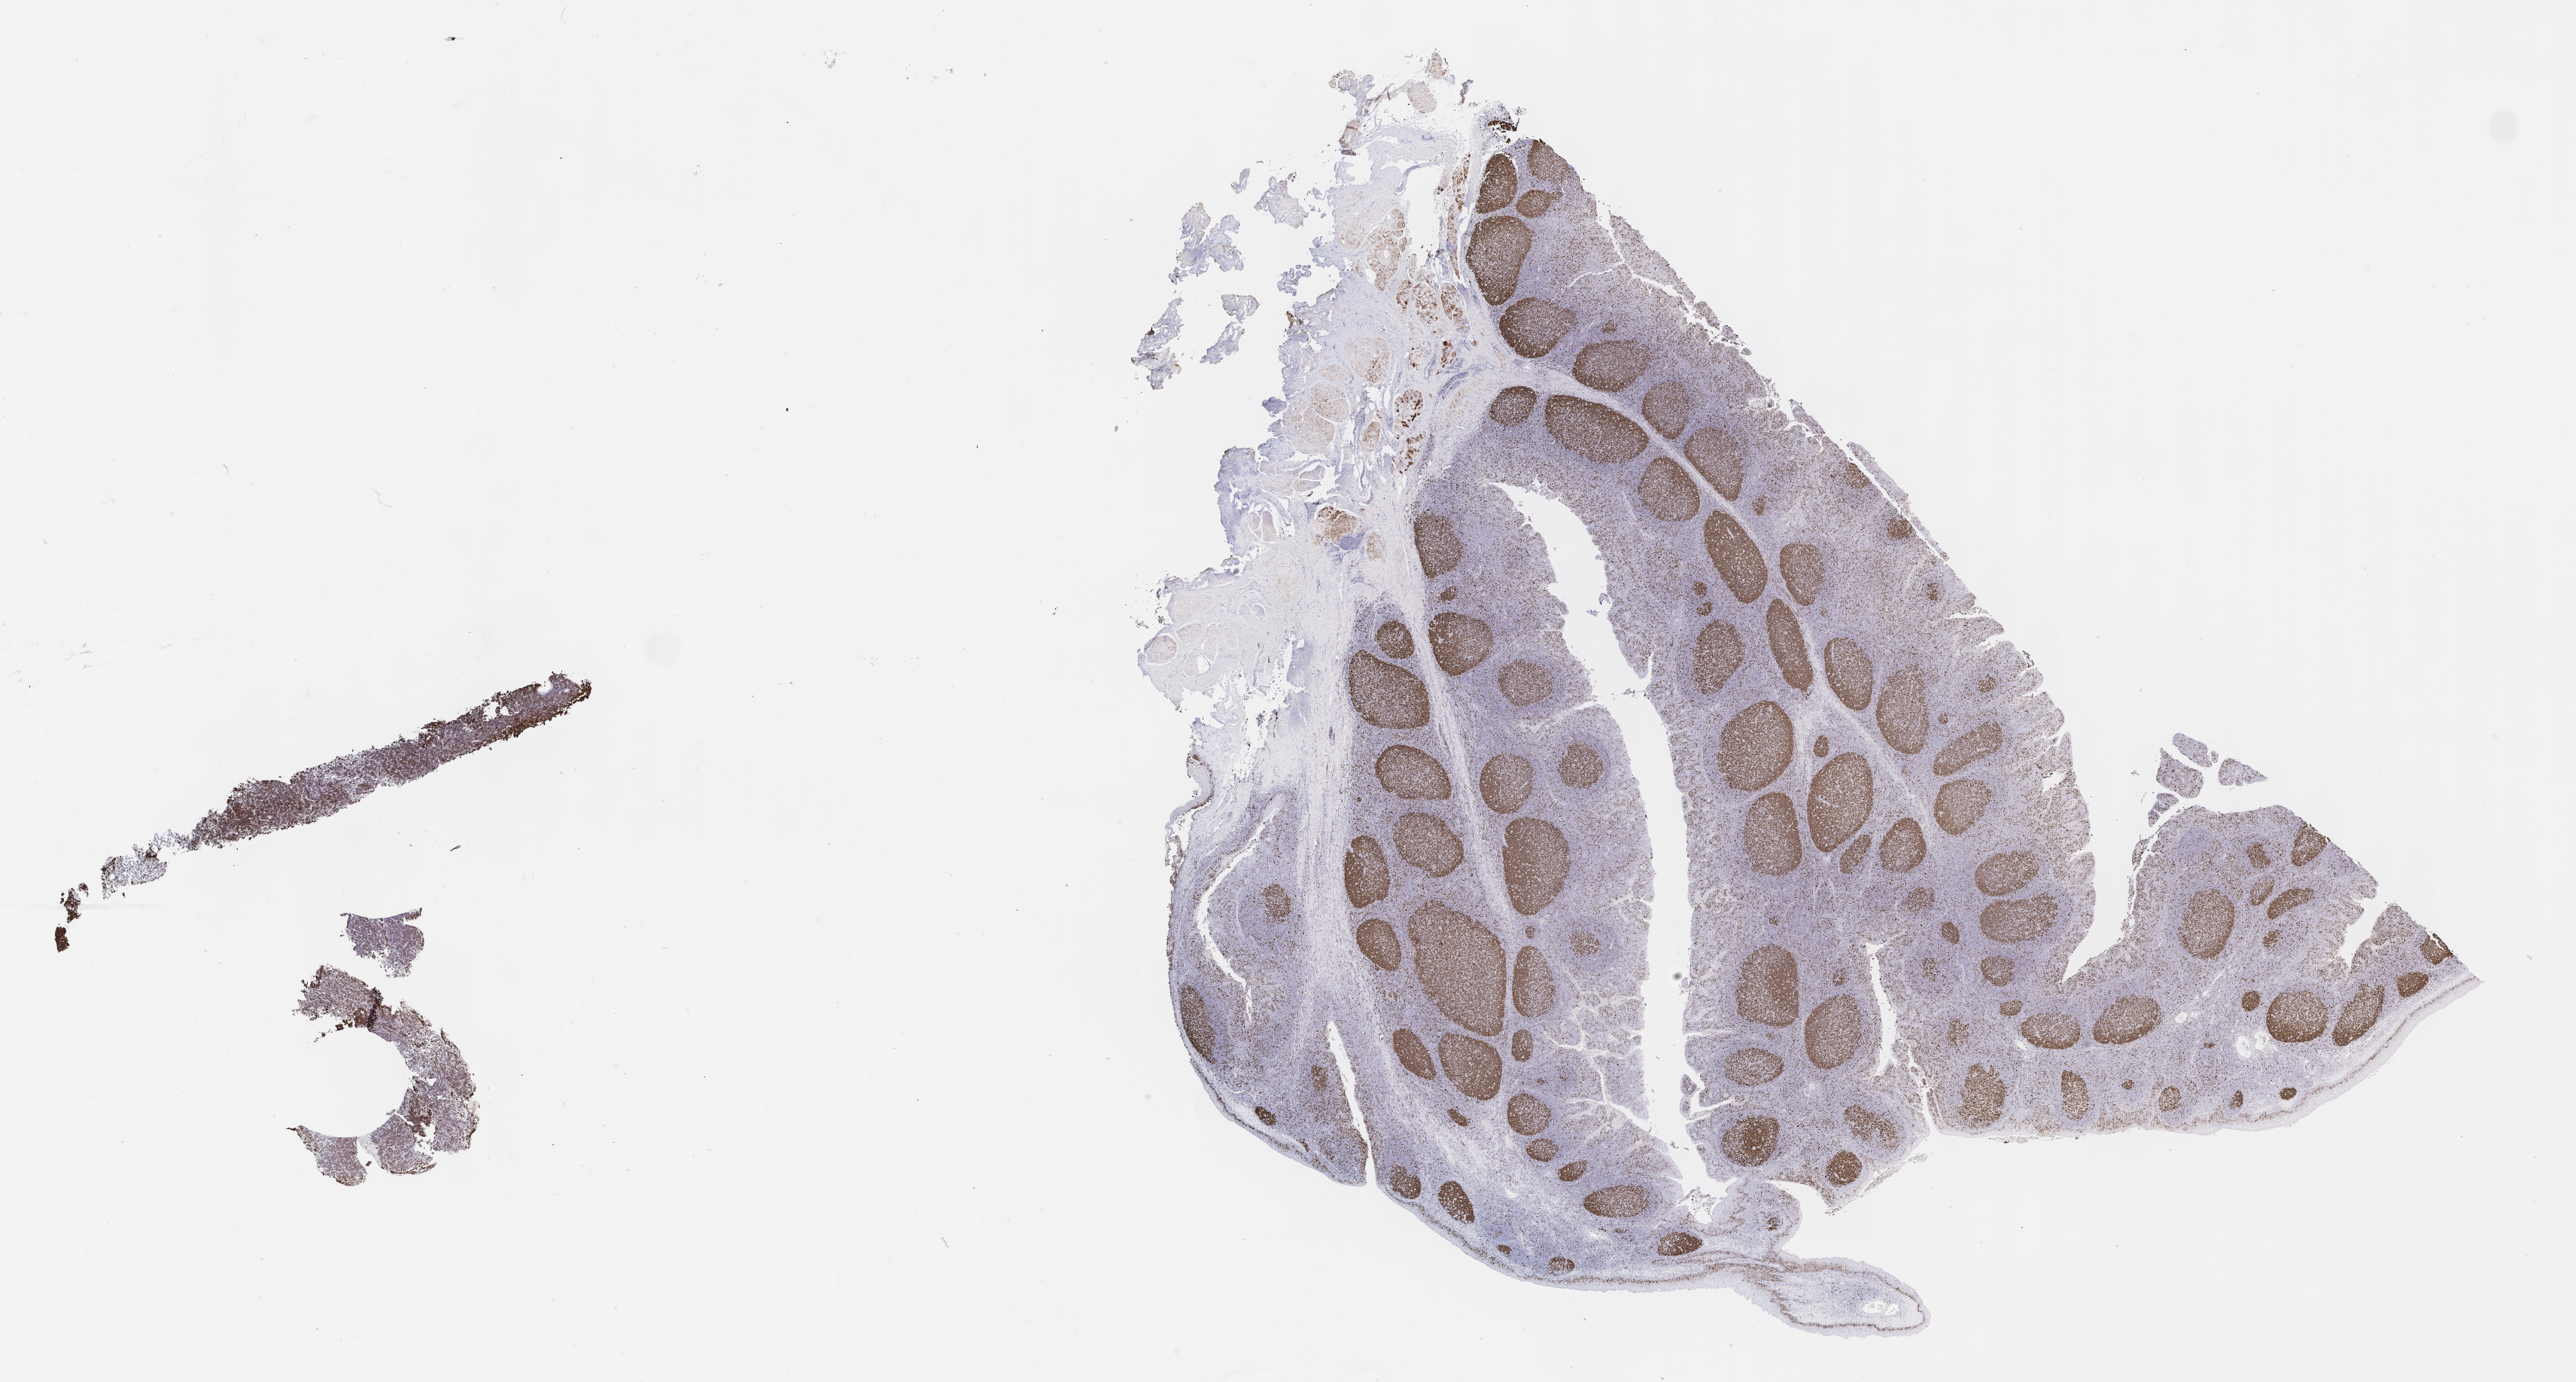
Whole-slide image, immunohistochemical stain for Ki-67, whole scanned area (about 27.7 x 14.8 mm) shown as a low-resolution overview. Tumor tissue. Anatomic site: ovary. Patient female; age 10 years.
* histologic diagnosis: Burkitt lymphoma, NOS